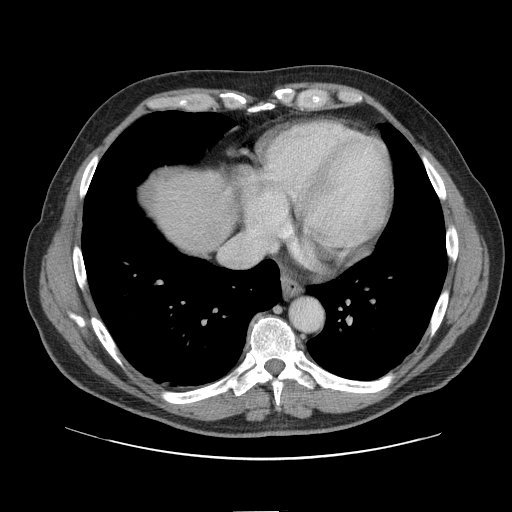
Contrast-enhanced abdominal CT, one axial slice. Soft-tissue window (W 400 / L 40 HU). 2.5 mm slice thickness. 512 × 512 image matrix. Male patient, age 66 years. From the clinical record (not read from this slice): diagnosis: colorectal cancer liver metastases, imaged before liver resection; multiple liver metastases: no; largest metastasis: 3.5 cm; disease in both lobes: no.
Outlined on this slice (expert manual segmentation):
- hepatic veins: bounding box (x1, y1, x2, y2) in pixels: (223, 243, 237, 258)
- liver: (152, 174, 236, 254)
- planned liver remnant (the part of the liver to remain after resection): (152, 174, 236, 254)
- liver metastasis: (212, 195, 218, 204)